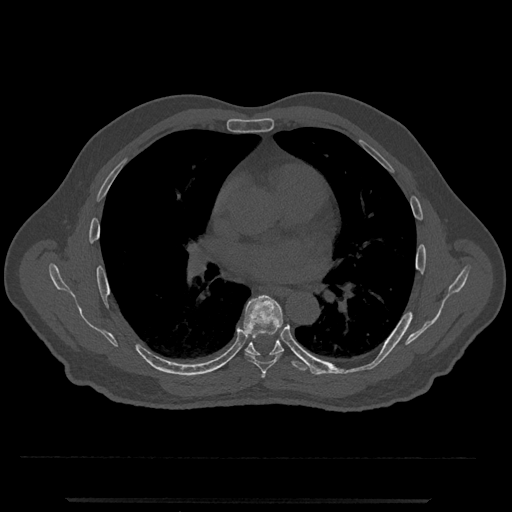
CT including the spine, one axial slice; position 715 of 797 along the scan axis; reconstruction kernel Br40s/3; 120 kVp; bone window (W 1800 / L 400 HU); 512 × 512 image matrix, field of view 419 × 419 mm. Male patient, age 63 years. From the clinical record (not read from this slice): primary cancer: prostate.
Outlined on this slice (semi-automatically segmented with operator editing):
- T5 vertebra: bounding box <262,372,266,378> (left, top, right, bottom; pixels)
- T6 vertebra: <243,295,283,374>
- T7 vertebra: <226,333,327,375>